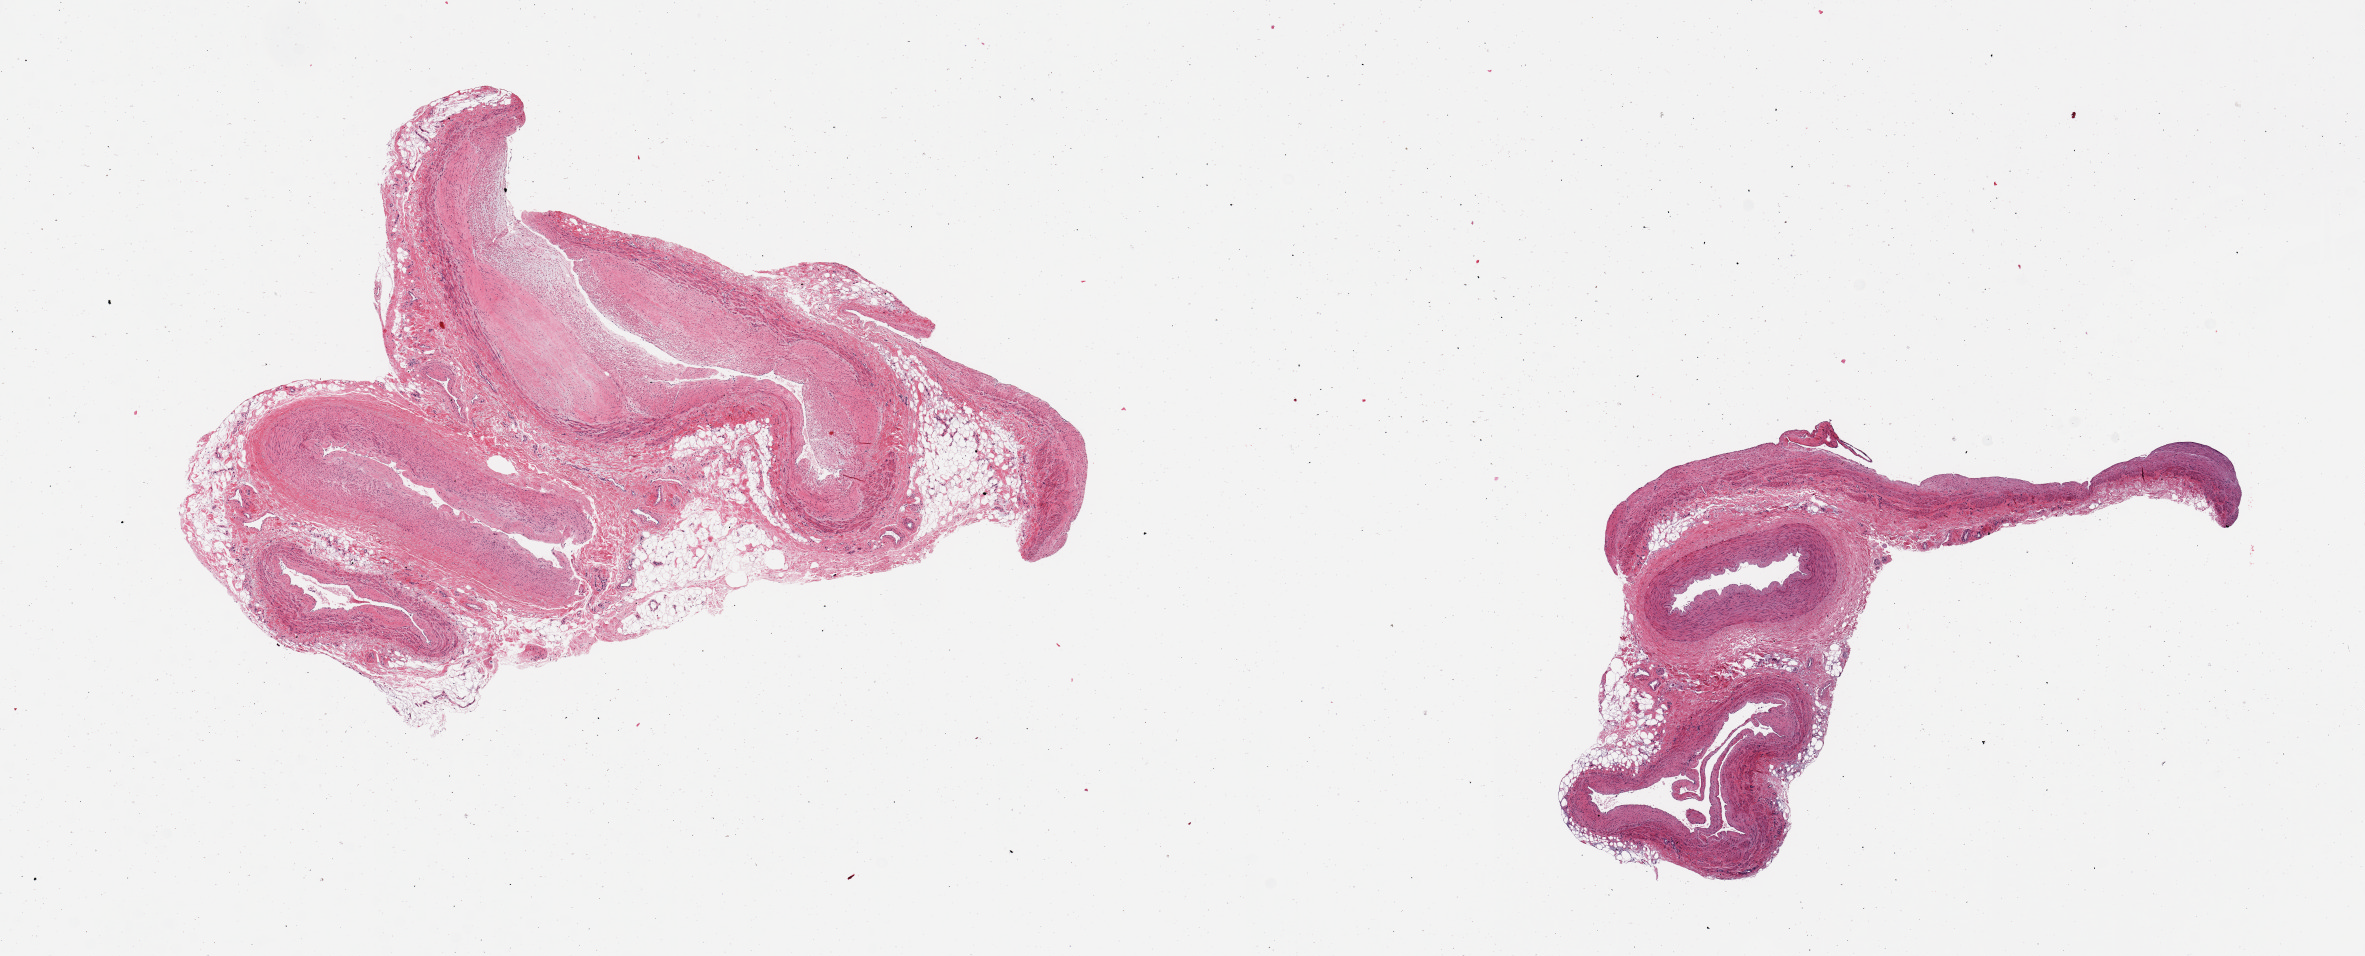
Digitized haematoxylin and eosin-stained section, a low-resolution overview of the entire scanned area, about 18.7 x 7.6 mm; PAXgene-fixed, paraffin-embedded tissue; section of tibial artery (target tissue); tissue donor sample. Donor sex: male.
Reviewer comment on this tissue sample: 2 pieces; several arteries, some with some without plaques.